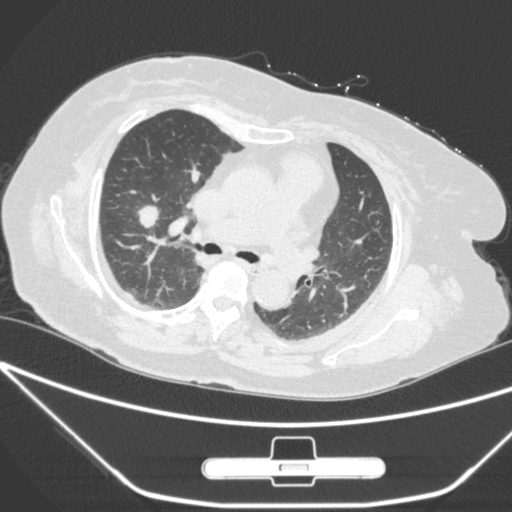
Chest CT, one axial slice. Slice 163 of 245 in the series (ordered by position). 120 kVp. Lung window (W 1500 / L -600 HU). 512 × 512 image matrix, field of view 365 × 365 mm. Patient: female, 65 years. From the clinical record (not read from this slice): clinical TNM (as recorded): T1c N0 M0; histopathological grade: G3.
Annotated regions visible in this slice (bounding box drawn by a radiologist):
- lung tumour (recorded histology: adenocarcinoma): bounding box [x1, y1, x2, y2] px = [130, 192, 166, 237]